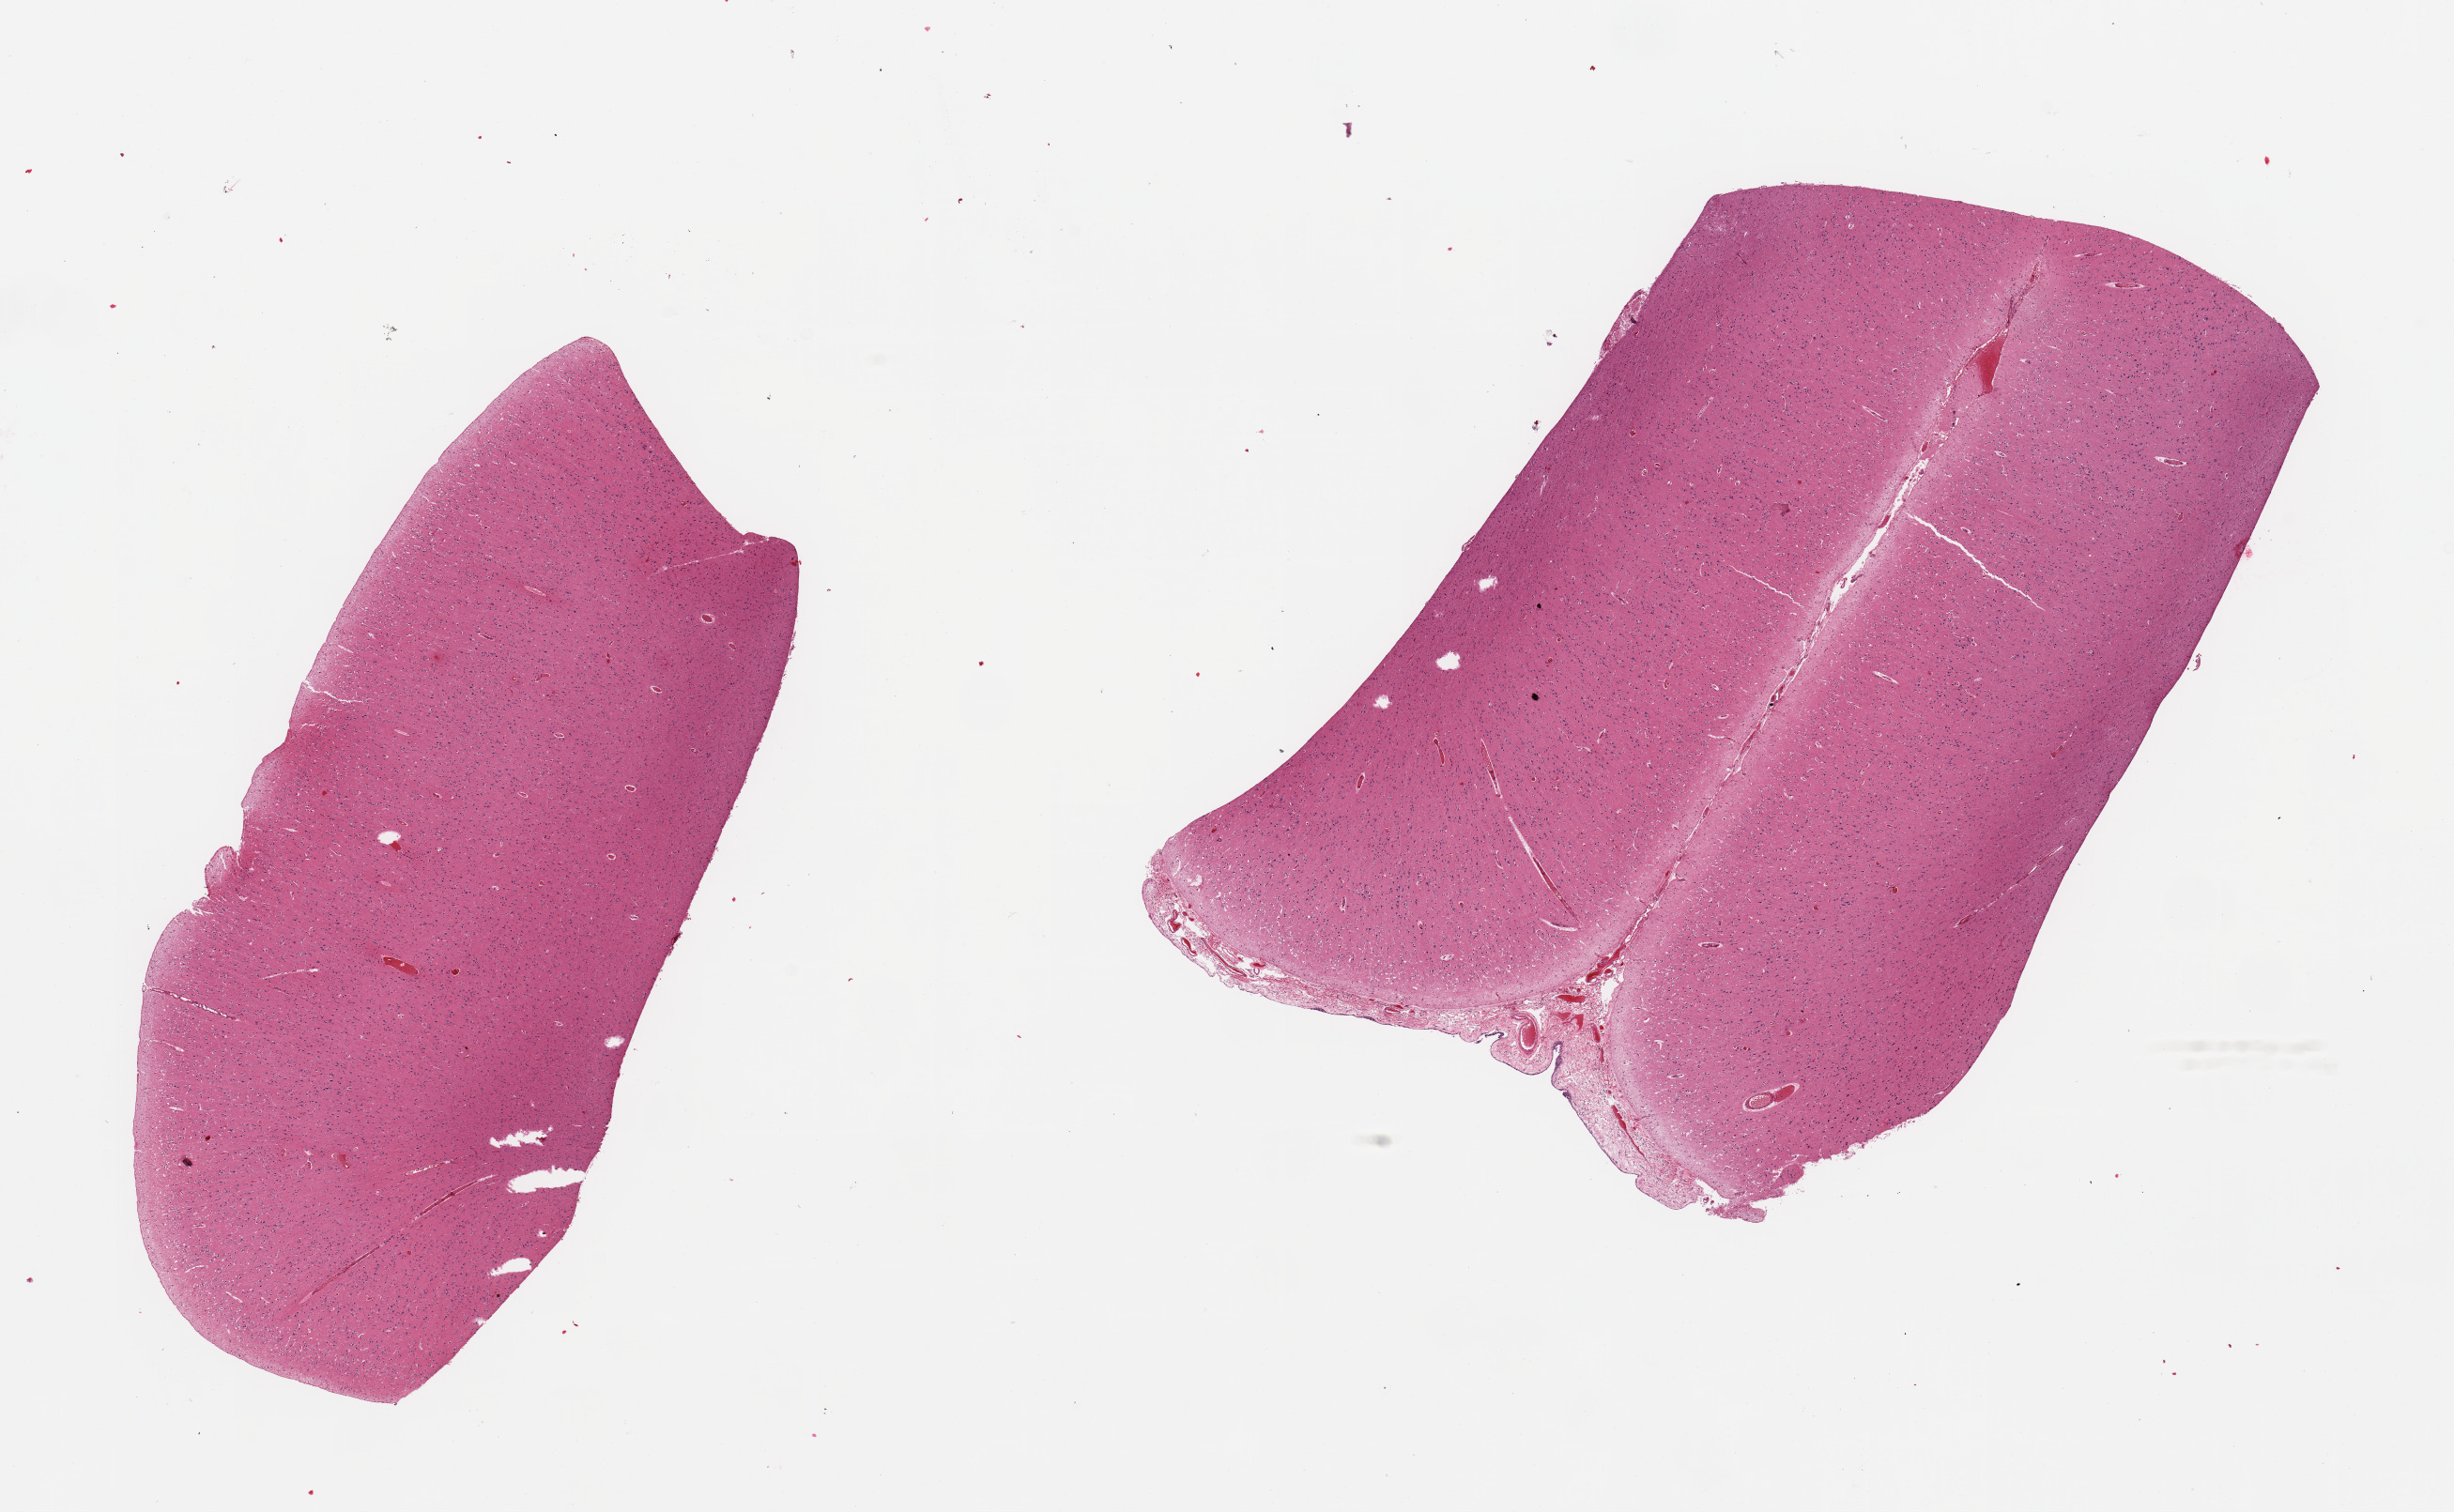
Digitized H&E-stained section, brightfield — a low-resolution overview of the entire scanned area, about 20.7 x 12.7 mm (slide scanned at 20x), PAXgene-fixed, paraffin-embedded tissue, target tissue: cerebral cortex, donor tissue sample. Male donor.
Reviewer comment on this tissue sample: 2 pieces; meninges along 1 edge.